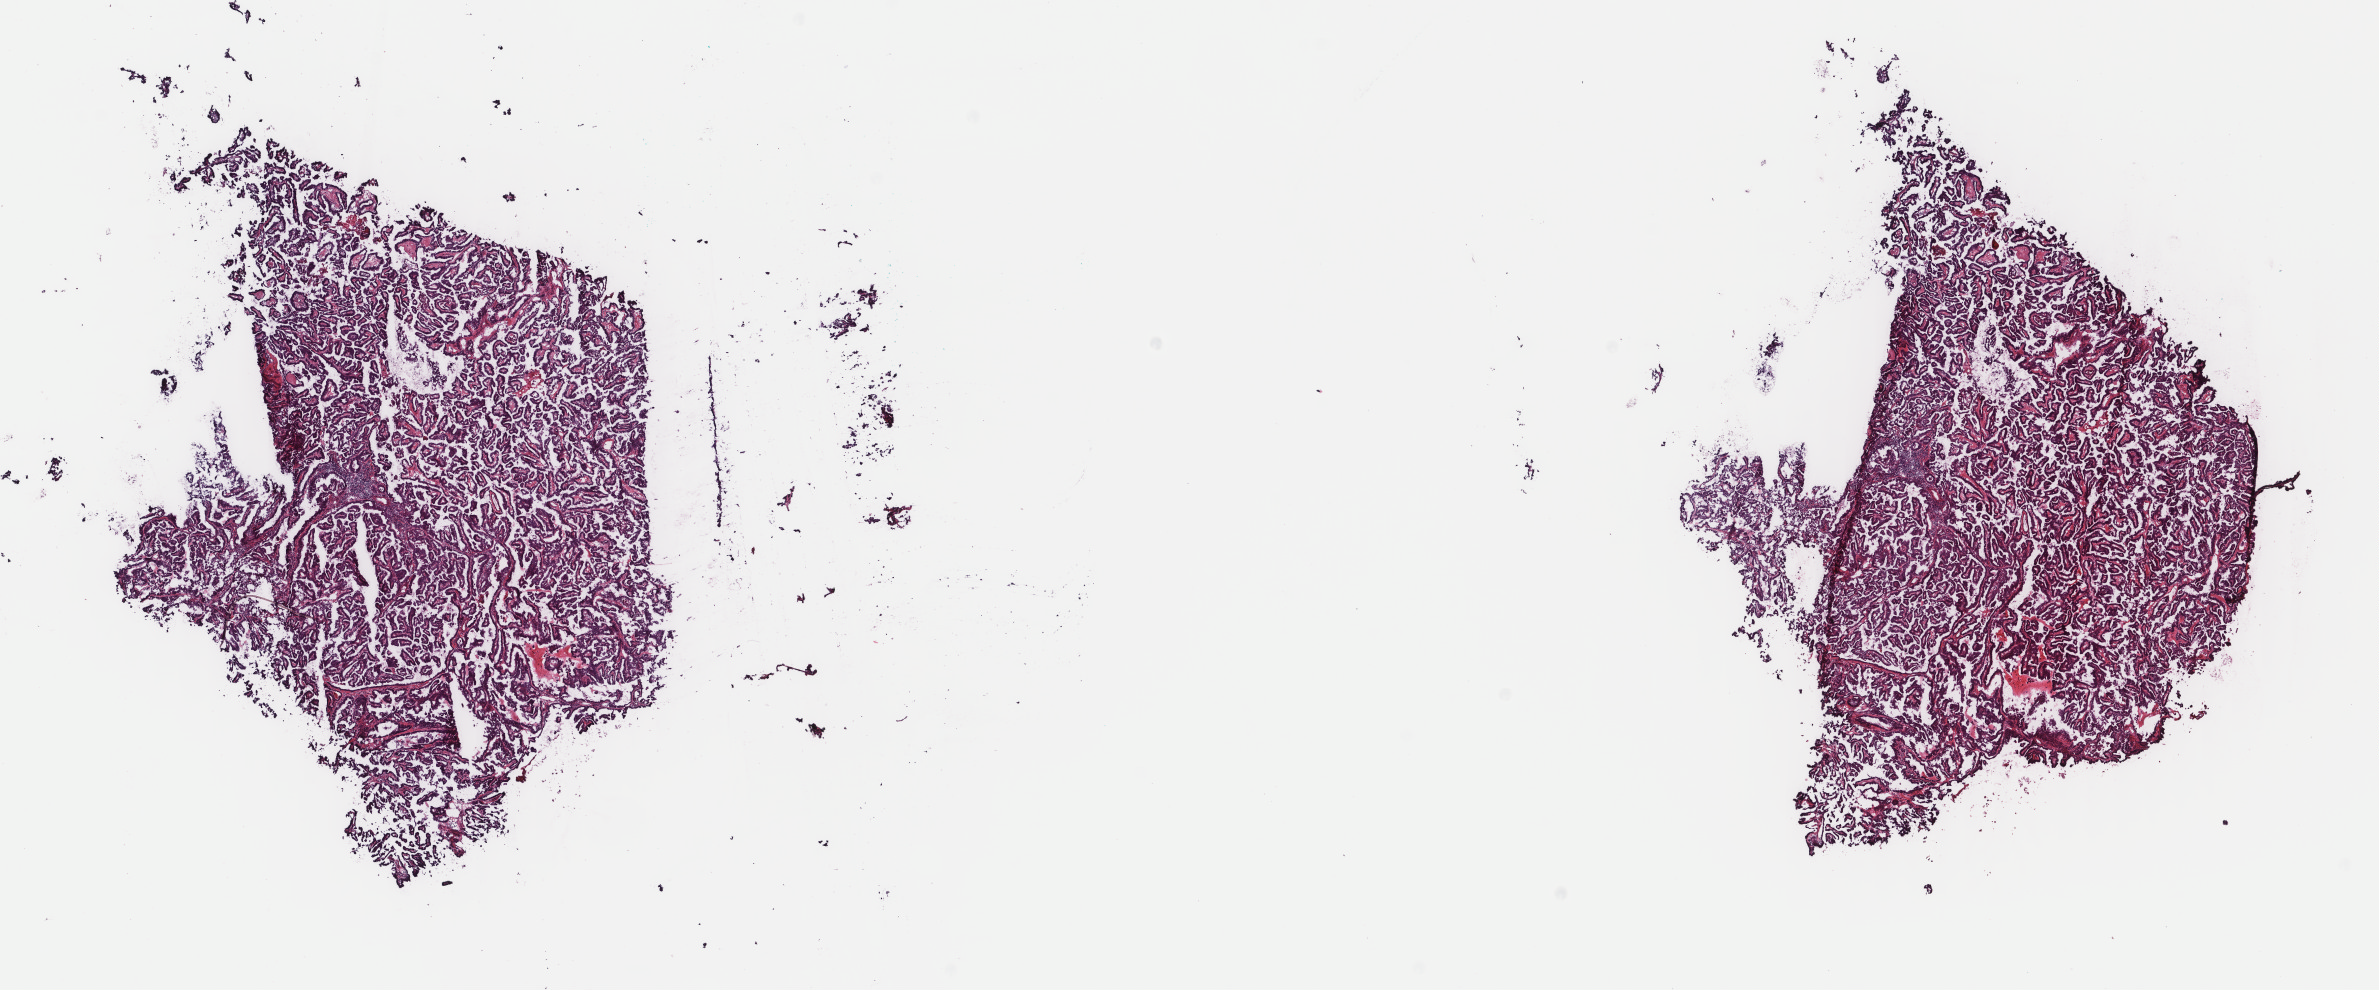
H&E whole-slide image, shown as a low-resolution overview of the whole scanned area (about 18.9 x 7.9 mm); frozen section; sample: primary tumour, thyroid. Male patient; age at initial diagnosis 64 years. Slide review estimates, as recorded: tumour cells 100%, tumour nuclei 90%.
Histologic diagnosis: Papillary carcinoma, columnar cell (thyroid gland).